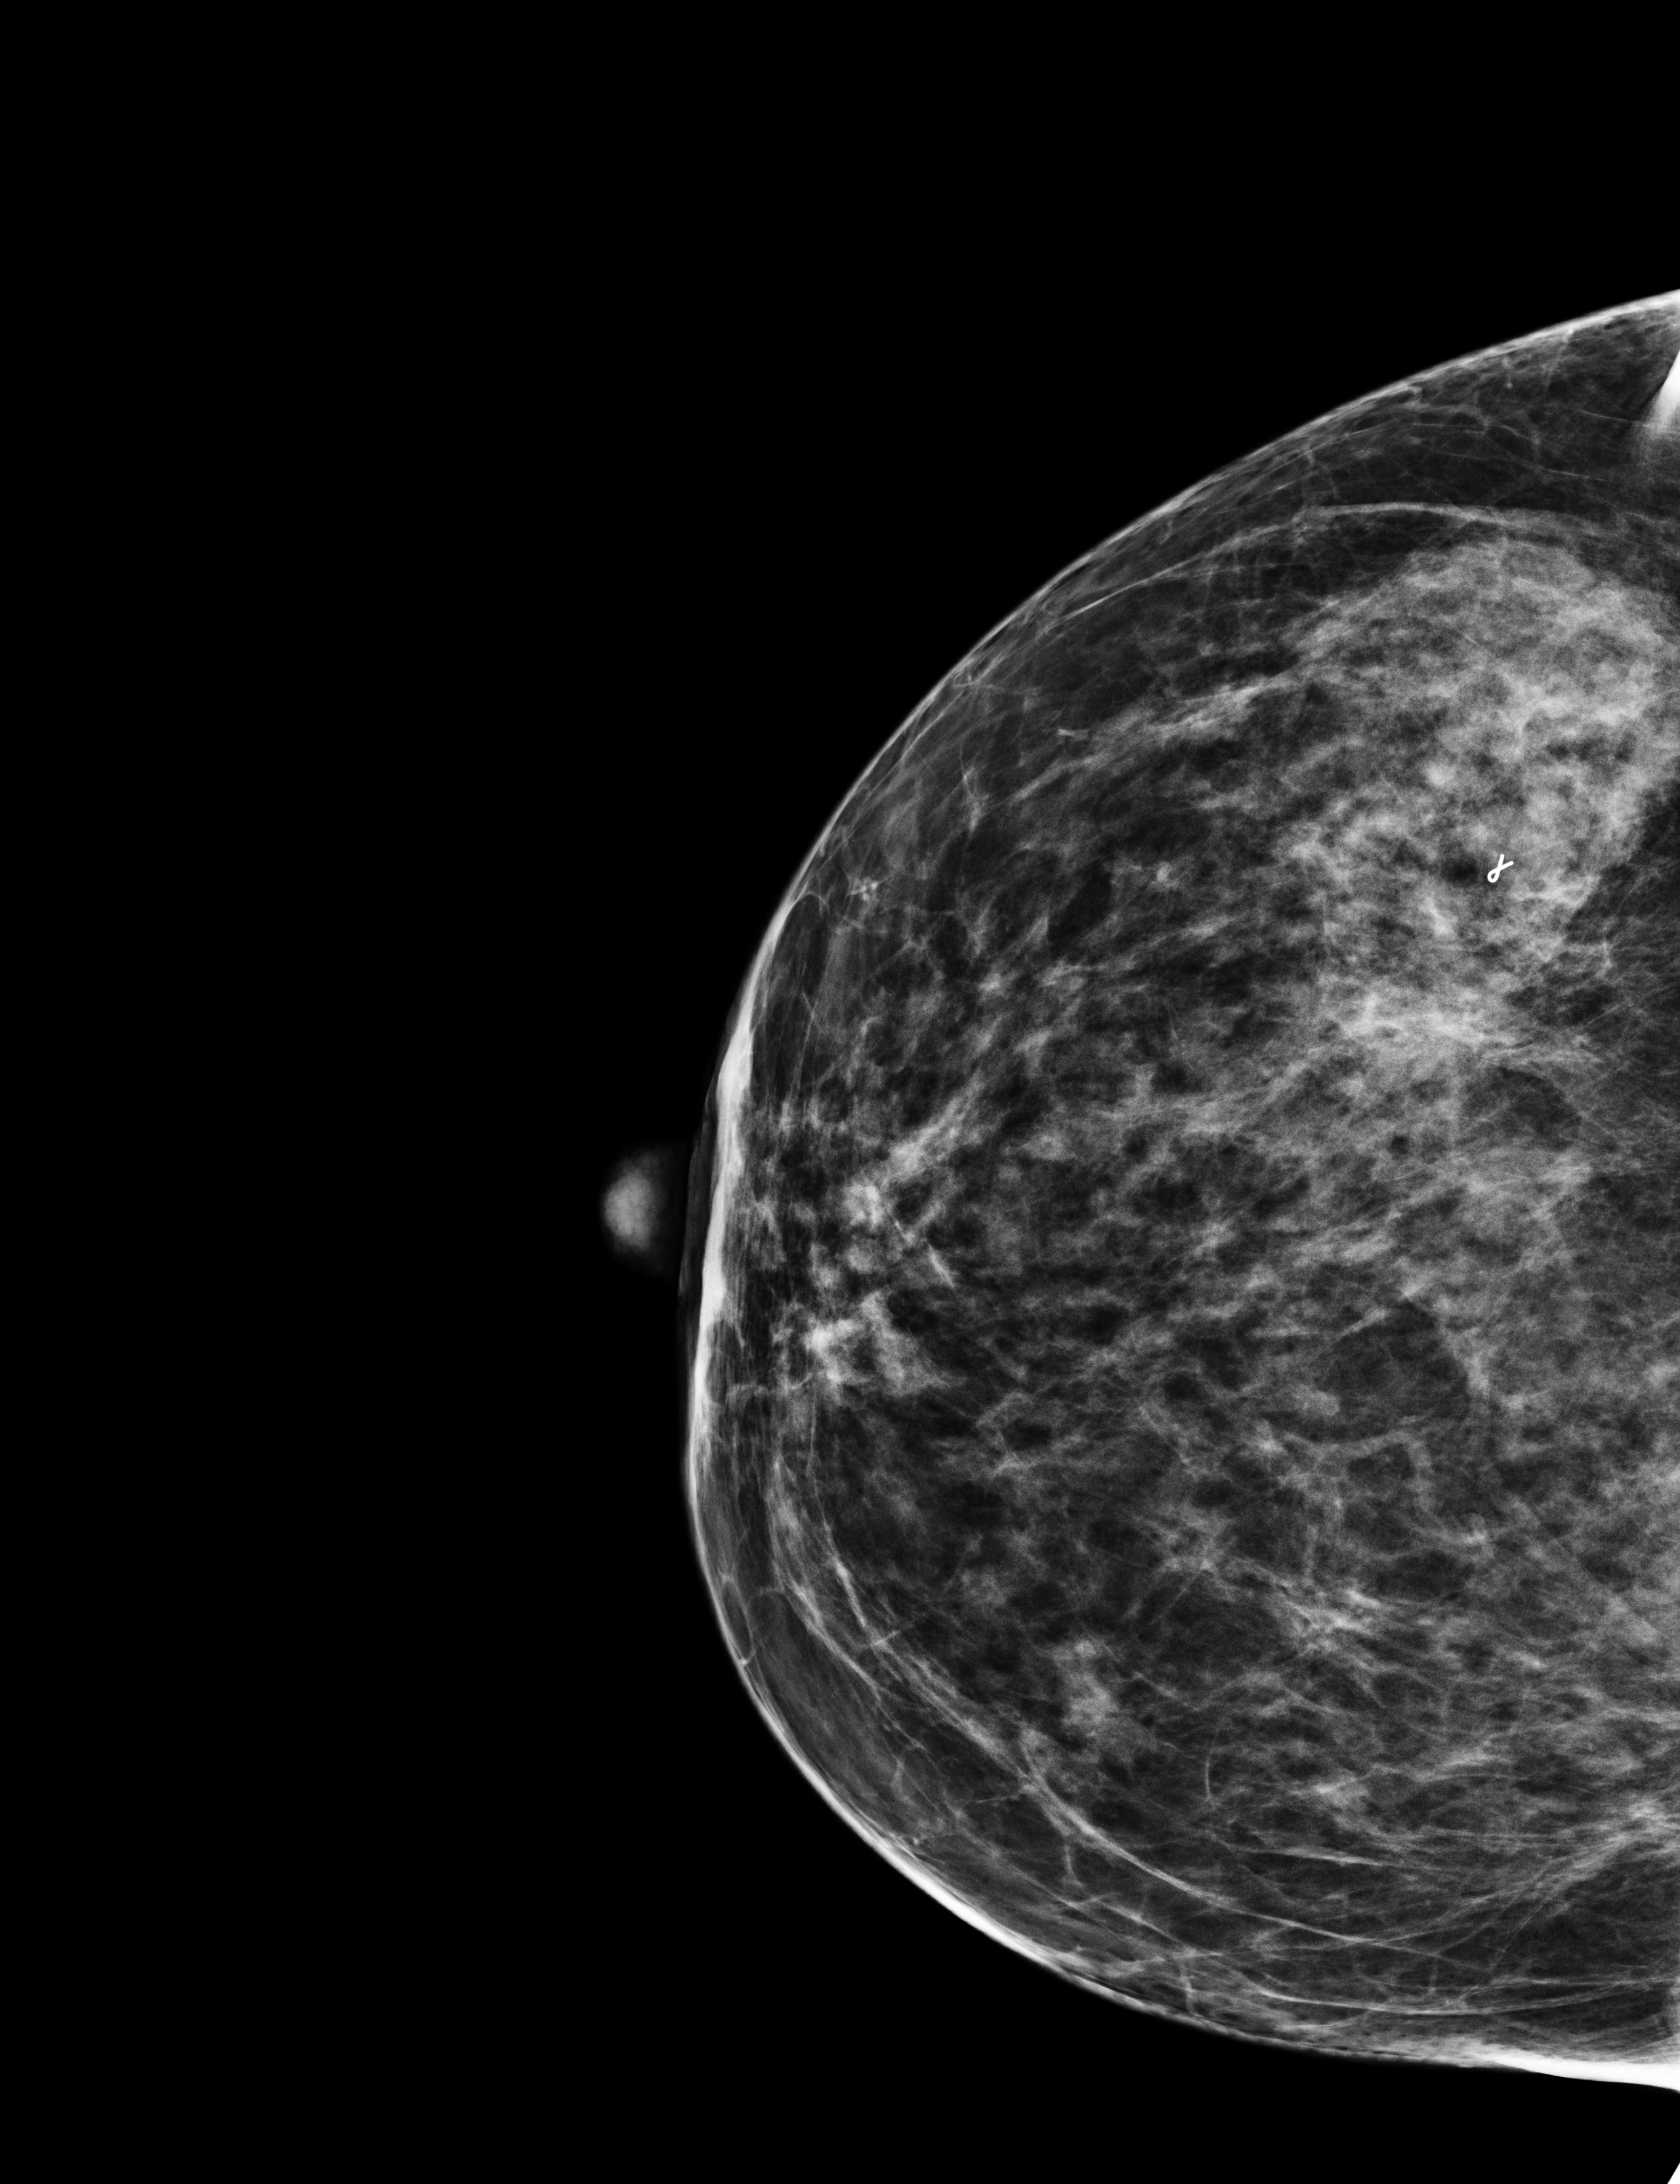
Digital mammogram (FFDM), right breast, CC view, screening examination, compressed breast thickness 56 mm. Patient: female, 62 years.
Breast density at the screening exam (both breasts): heterogeneously dense (BI-RADS density category c). Final BI-RADS assessment for this screening round (tomosynthesis exam, both breasts): category 1. Recall: no recall after this screen.